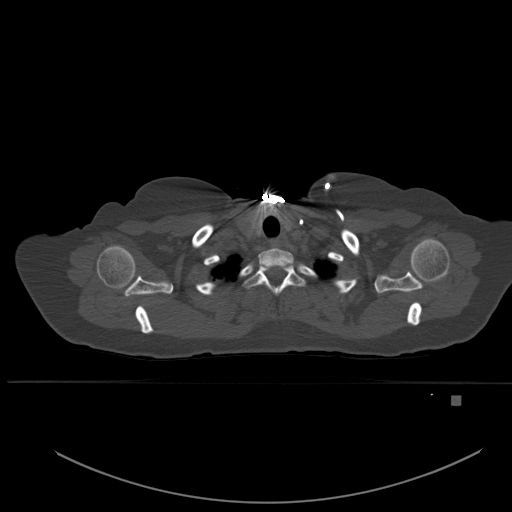
CT including the spine, one axial slice; bone window (W 1800 / L 400 HU); 1.5 mm slice thickness; 512 × 512 image matrix. Patient: female, 49 years. Case-level facts recorded for this patient, not image findings: primary cancer: breast; vertebrae with lytic lesions (as recorded): L3, T12, L4.
Outlined on this slice (semi-automatically segmented with operator editing):
- T1 vertebra: box from (x=244, y=264) to (x=305, y=296) px